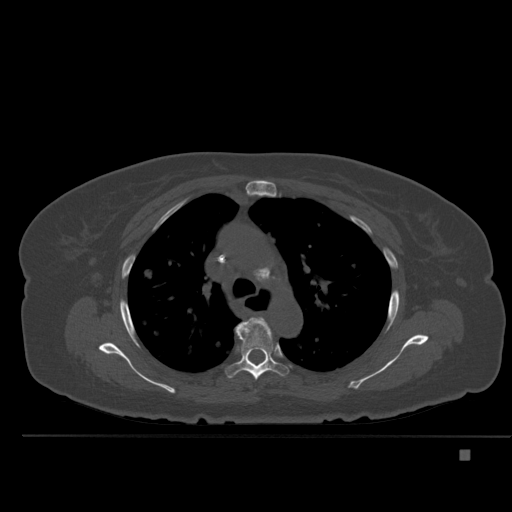
CT including the spine, one axial slice. Slice 356 of 477 in the series (ordered by position). Bone window (W 1800 / L 400 HU). 1.5 mm slice thickness. 512 × 512 image matrix, field of view 422 × 422 mm. Female patient, age 74 years. Case-level facts recorded for this patient, not image findings: primary cancer: colon.
Structures marked on this image (semi-automatically segmented with operator editing):
- T4 vertebra: bounding box [x1, y1, x2, y2] px = [246, 318, 266, 323]
- T5 vertebra: [228, 317, 287, 380]